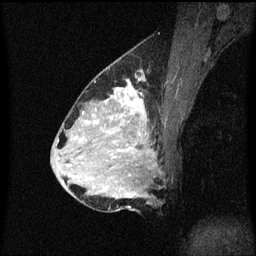
Breast MRI (dynamic contrast-enhanced), one sagittal slice. Slice 30 of 60 in the series (ordered by position). Dynamic contrast-enhanced series, image 2 of 3 at this slice position (ordered by acquisition). 1.5 T. TE 4.2 ms, TR 8.4 ms. 2 mm slice thickness. 256 × 256 image matrix, field of view 200 × 200 mm. Female patient, age 34 years. Case-level facts recorded for this patient, not image findings: setting: breast cancer imaged before/during neoadjuvant chemotherapy; receptor status: HR-positive, HER2-negative.
Annotated regions visible in this slice (semi-automatically segmented with operator editing):
- analysis volume of interest (the breast-tissue region the enhancement analysis was run in; not a lesion): box from (x=69, y=70) to (x=163, y=209) px
- tumour enhancement mask (voxels above the 70 % enhancement threshold inside the analysis volume of interest): (x=110, y=88)–(x=146, y=151)